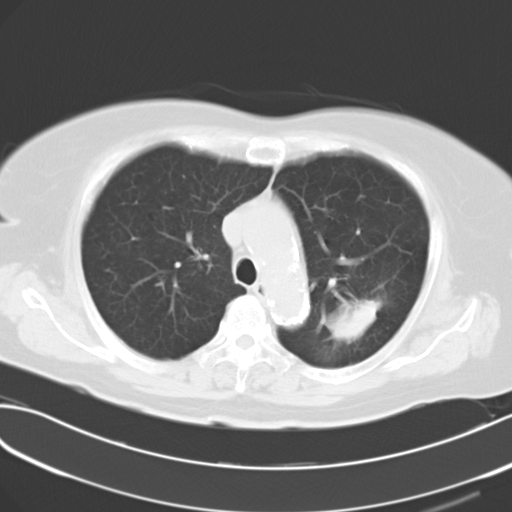
Chest CT, one axial slice. Position 25 of 30 along the scan axis. Reconstruction kernel B40f. 120 kVp. Lung window (W 1500 / L -600 HU). 10 mm slice thickness. 512 × 512 image matrix, field of view 353 × 353 mm. Female patient, age 70 years. Case-level facts recorded for this patient, not image findings: clinical TNM (as recorded): T2 N0 M0.
Annotated regions visible in this slice (rectangle marked by the reading radiologist):
- lung tumour (recorded histology: adenocarcinoma): bounding box <331,296,377,342> (left, top, right, bottom; pixels)